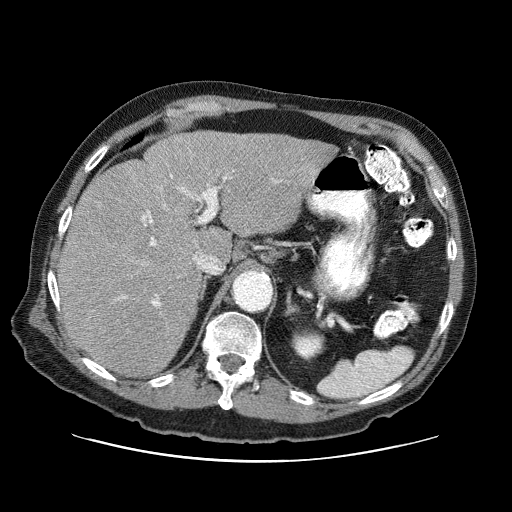
Contrast-enhanced abdominal CT (liver protocol), one axial slice; 120 kVp; one of 3 acquisitions stored at this slice position; soft-tissue window (W 400 / L 40 HU); 512 × 512 image matrix, field of view 400 × 400 mm. Case-level facts recorded for this patient, not image findings: diagnosis: hepatocellular carcinoma (patient treated with transarterial chemoembolisation; whether this scan precedes or follows treatment is not stated here); TNM stage (as recorded): Stage-IIIA; Child-Pugh class: A; tumour differentiation: well differentiated; tumour size: 6 cm.
Outlined on this slice (semi-automatically segmented with operator editing):
- liver parenchyma outside the tumour (the mass and vessels are separate outlines, so this box may not span the whole liver): bounding box [x1, y1, x2, y2] px = [58, 132, 332, 376]
- liver vessels: [118, 175, 278, 306]